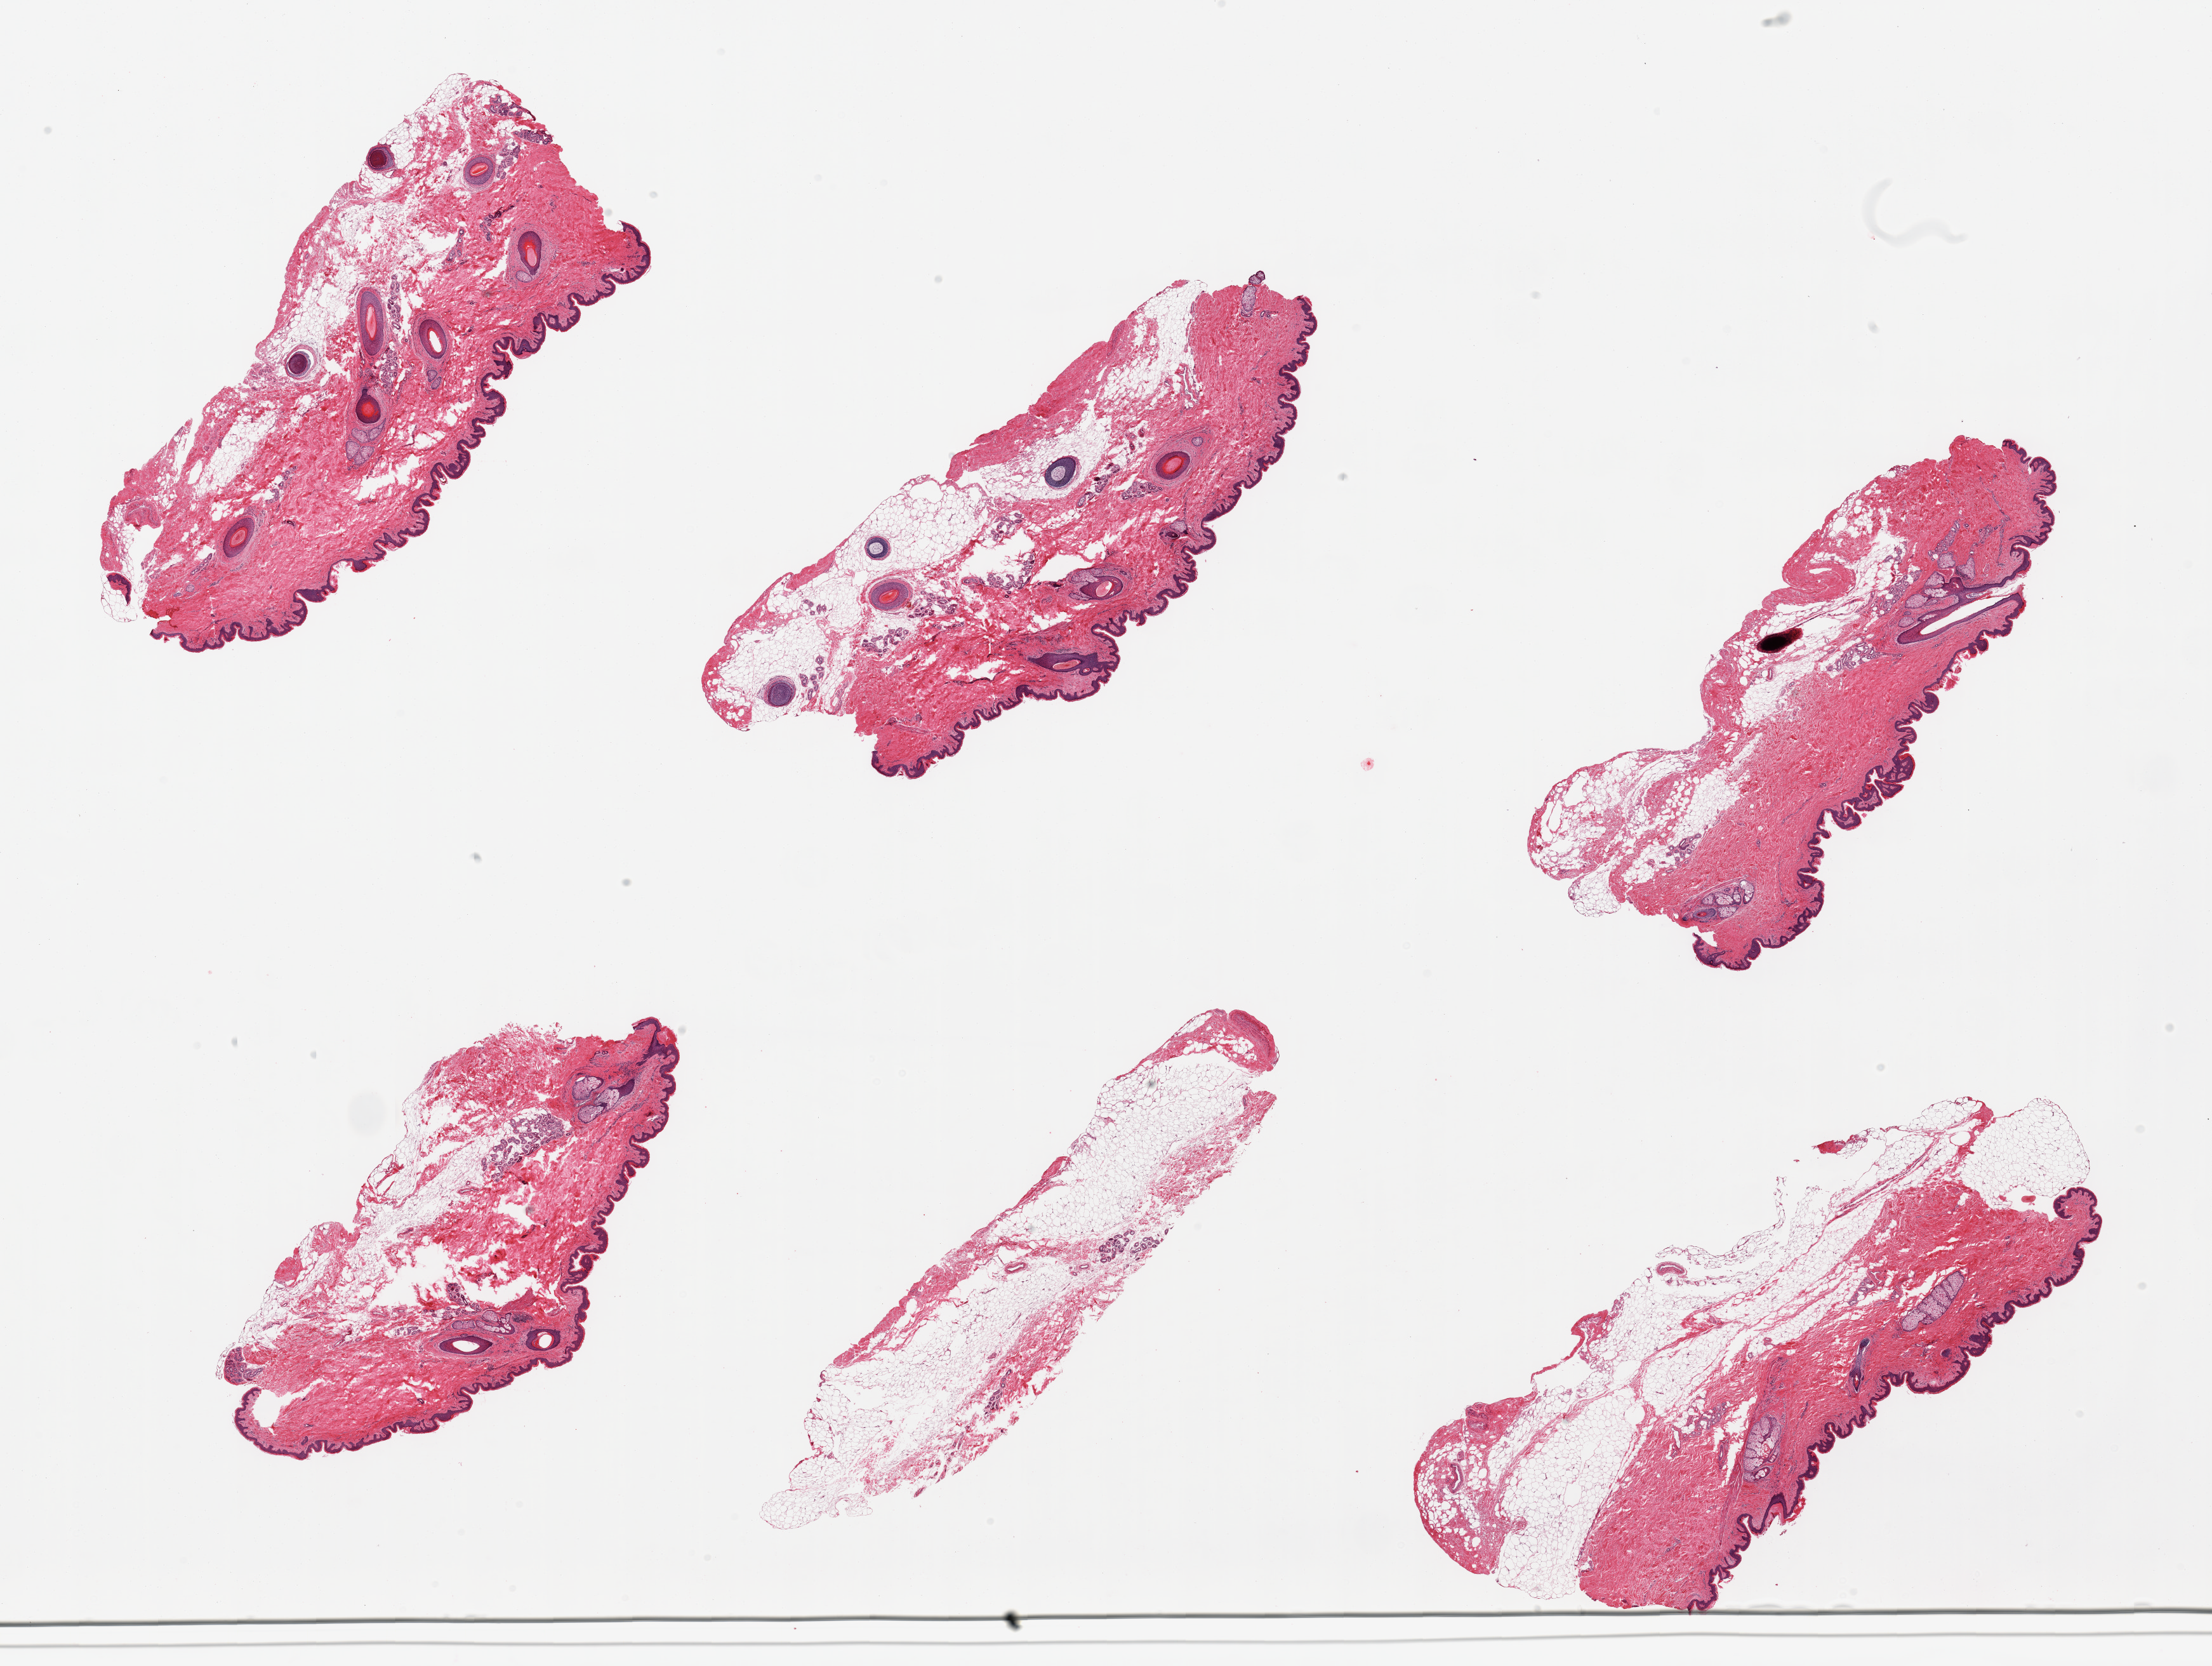
Whole-slide image, H&E stain, a low-resolution overview of the entire scanned area, about 27.6 x 20.8 mm (acquisition: 20x scan); PAXgene-fixed, paraffin-embedded tissue; section of skin of suprapubic region (target tissue); donor tissue sample. Donor: male.
• review note (as recorded): 6 pieces, squamous epithelium is ~45microns; adherent dermal fat ~1-1.5mm